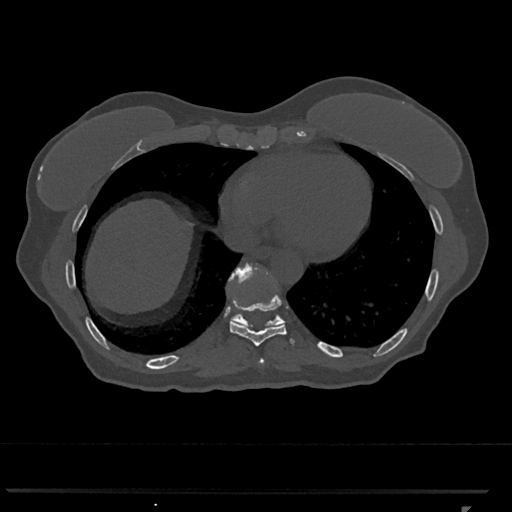
CT including the spine, one axial slice; slice 607 of 793 in the series (ordered by position); reconstruction kernel Br40s/3; bone window (W 1800 / L 400 HU); 0.5 mm slice thickness; 512 × 512 image matrix, field of view 380 × 380 mm. Female patient, age 62 years. From the clinical record (not read from this slice): primary cancer: renal.
Annotated regions visible in this slice (semi-automatic segmentation, software-assisted and operator-edited):
- T10 vertebra: bounding box [x1, y1, x2, y2] px = [229, 263, 285, 327]
- T8 vertebra: [259, 358, 265, 364]
- T9 vertebra: [230, 295, 295, 346]